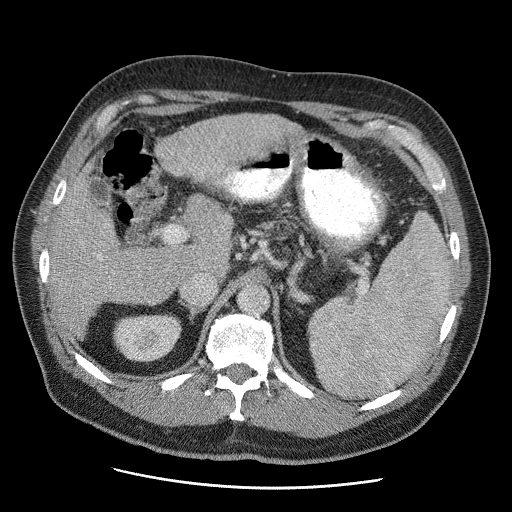
Contrast-enhanced abdominal CT (liver protocol), one axial slice. Slice 27 of 81 in the series (ordered by position). Soft-tissue window (W 400 / L 40 HU). 2.5 mm slice thickness. 512 × 512 image matrix. From the clinical record (not read from this slice): diagnosis: hepatocellular carcinoma (patient treated with transarterial chemoembolisation; whether this scan precedes or follows treatment is not stated here); TNM stage (as recorded): Stage-IIIA; Child-Pugh class: A; tumour differentiation: moderately differentiated; tumour size: 5.5 cm.
Outlined on this slice (semi-automatic segmentation, software-assisted and operator-edited):
- abdominal aorta: bounding box <239,286,268,315> (left, top, right, bottom; pixels)
- liver parenchyma outside the tumour (the mass and vessels are separate outlines, so this box may not span the whole liver): <52,114,300,317>